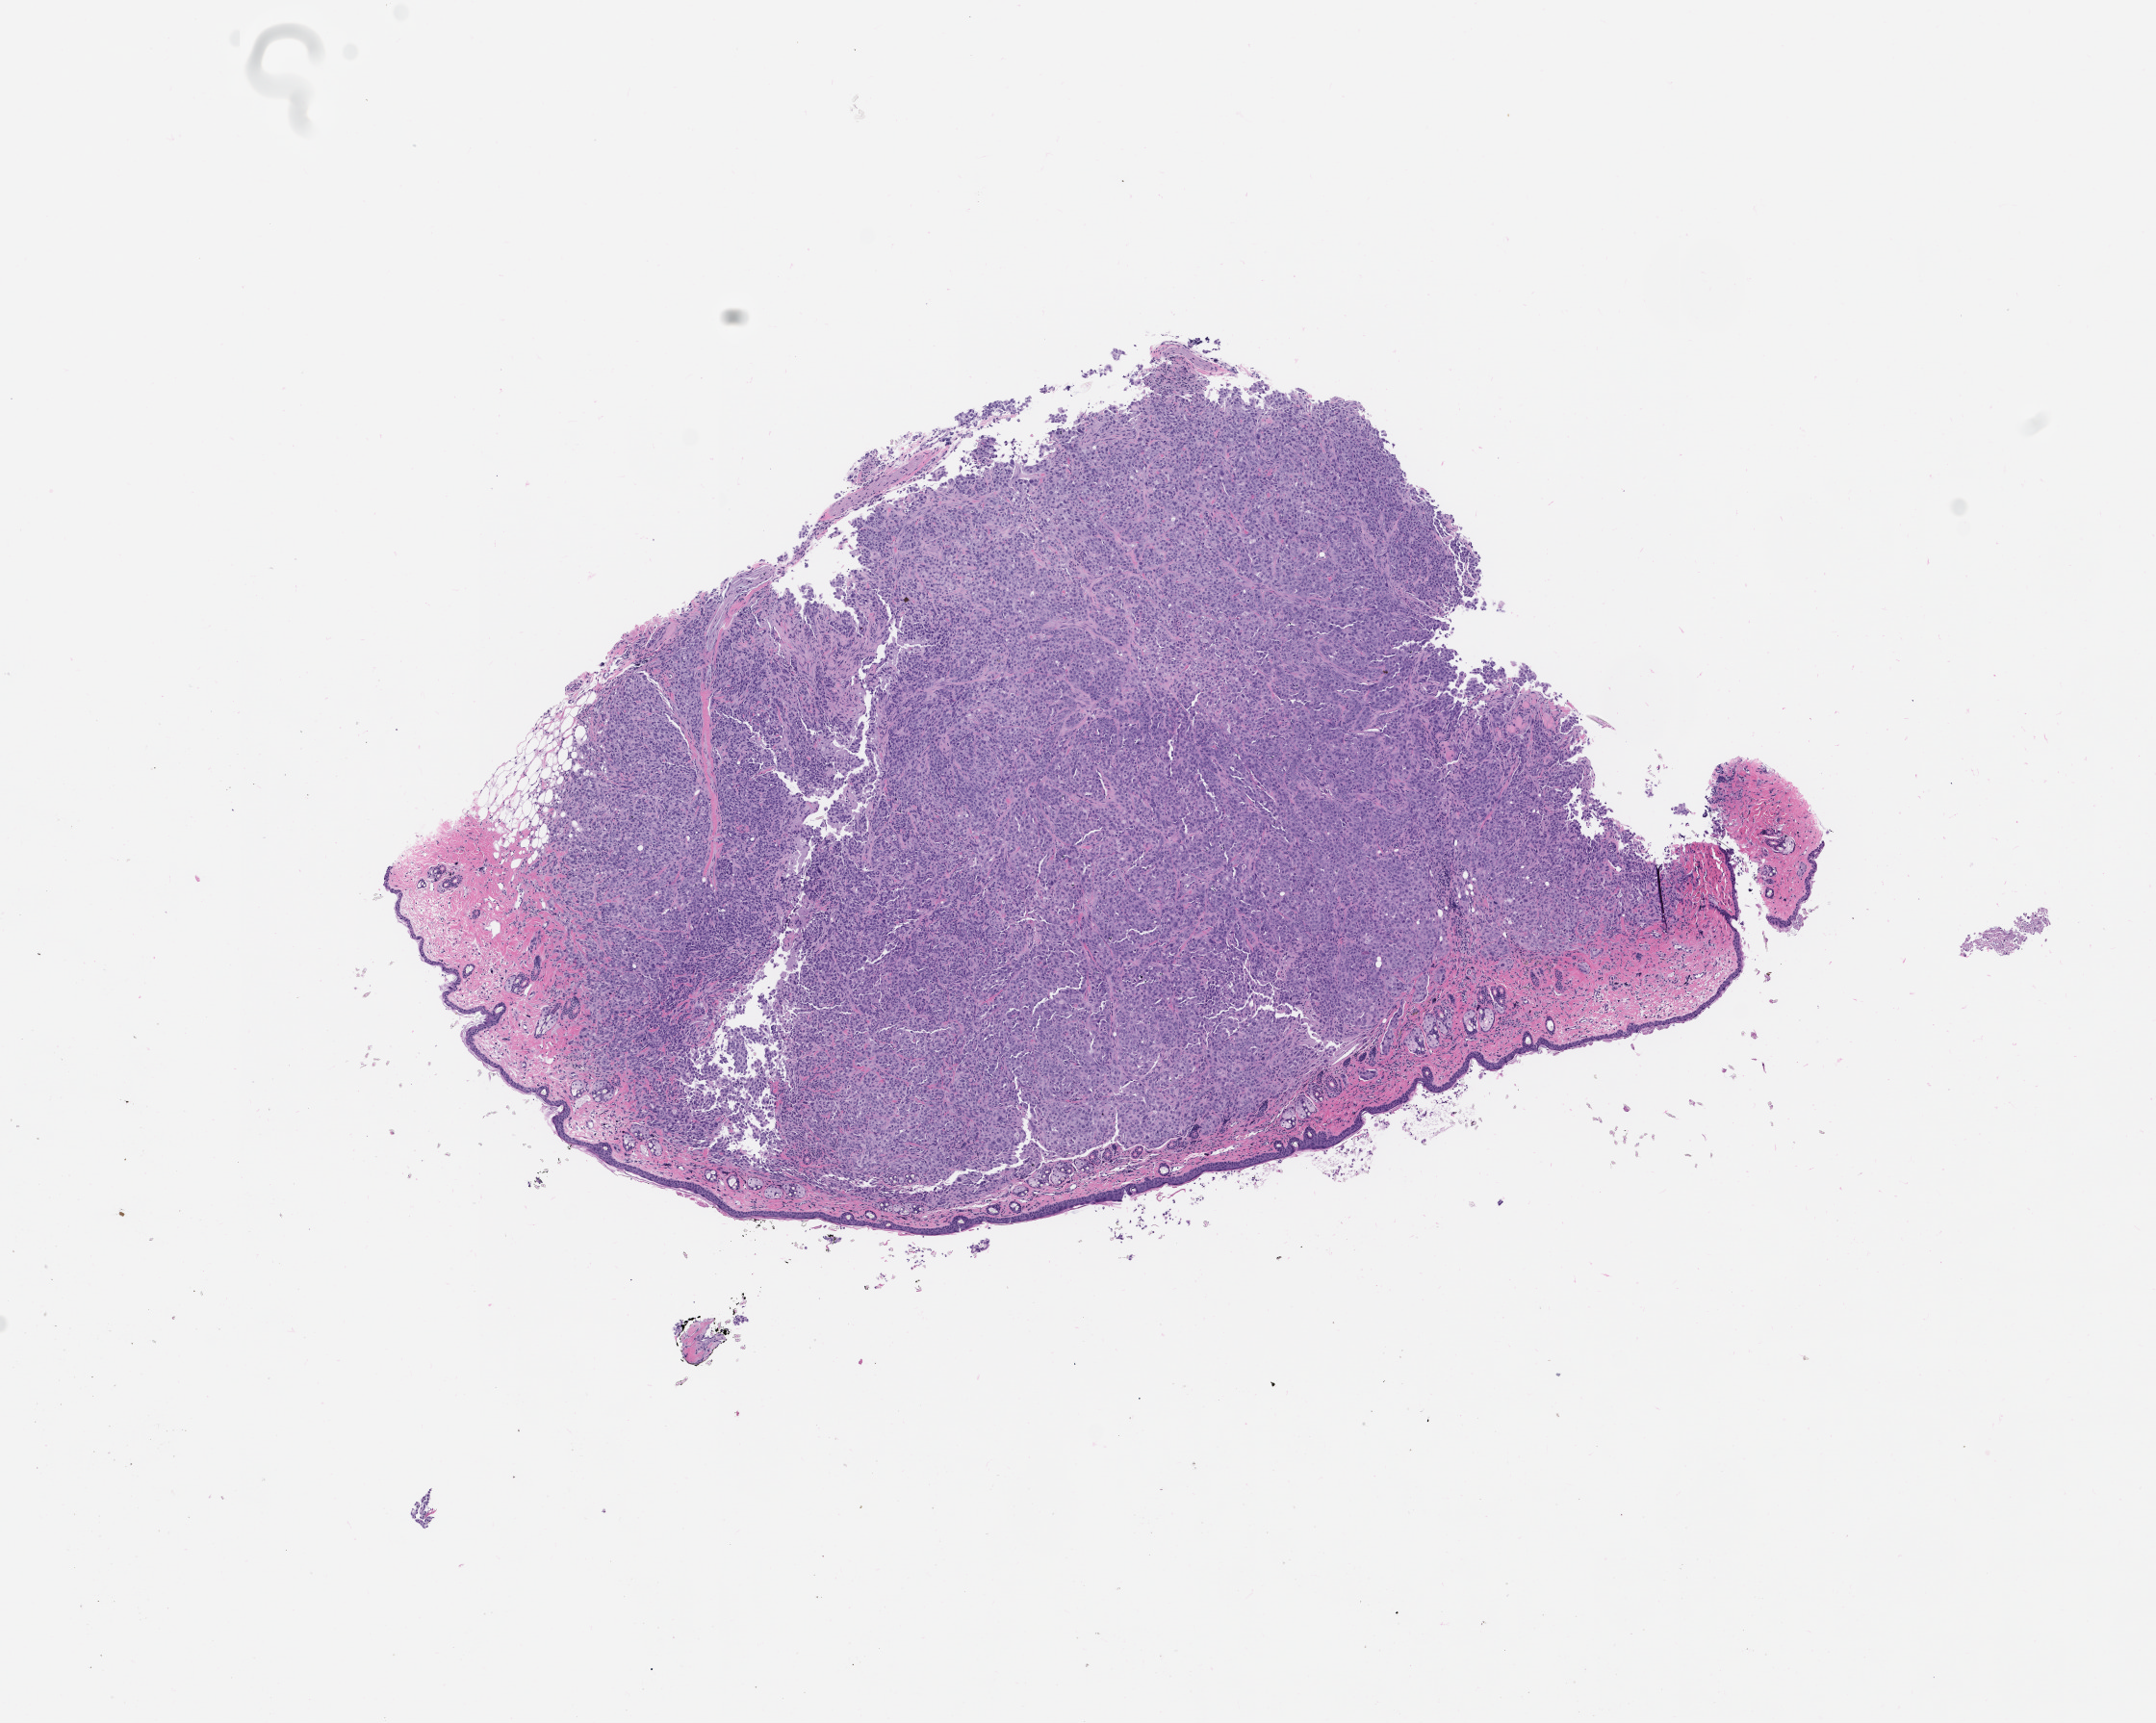
Whole-slide image, hematoxylin and eosin (H&E): patient-derived xenograft (human tumor grown in a mouse), passage 0 — low-resolution overview of the scanned area, about 9.0 x 7.2 mm, formalin-fixed, paraffin-embedded (FFPE) tissue, originating tumor site category: lung.
Originating patient diagnosis: Lung Adenocarcinoma.